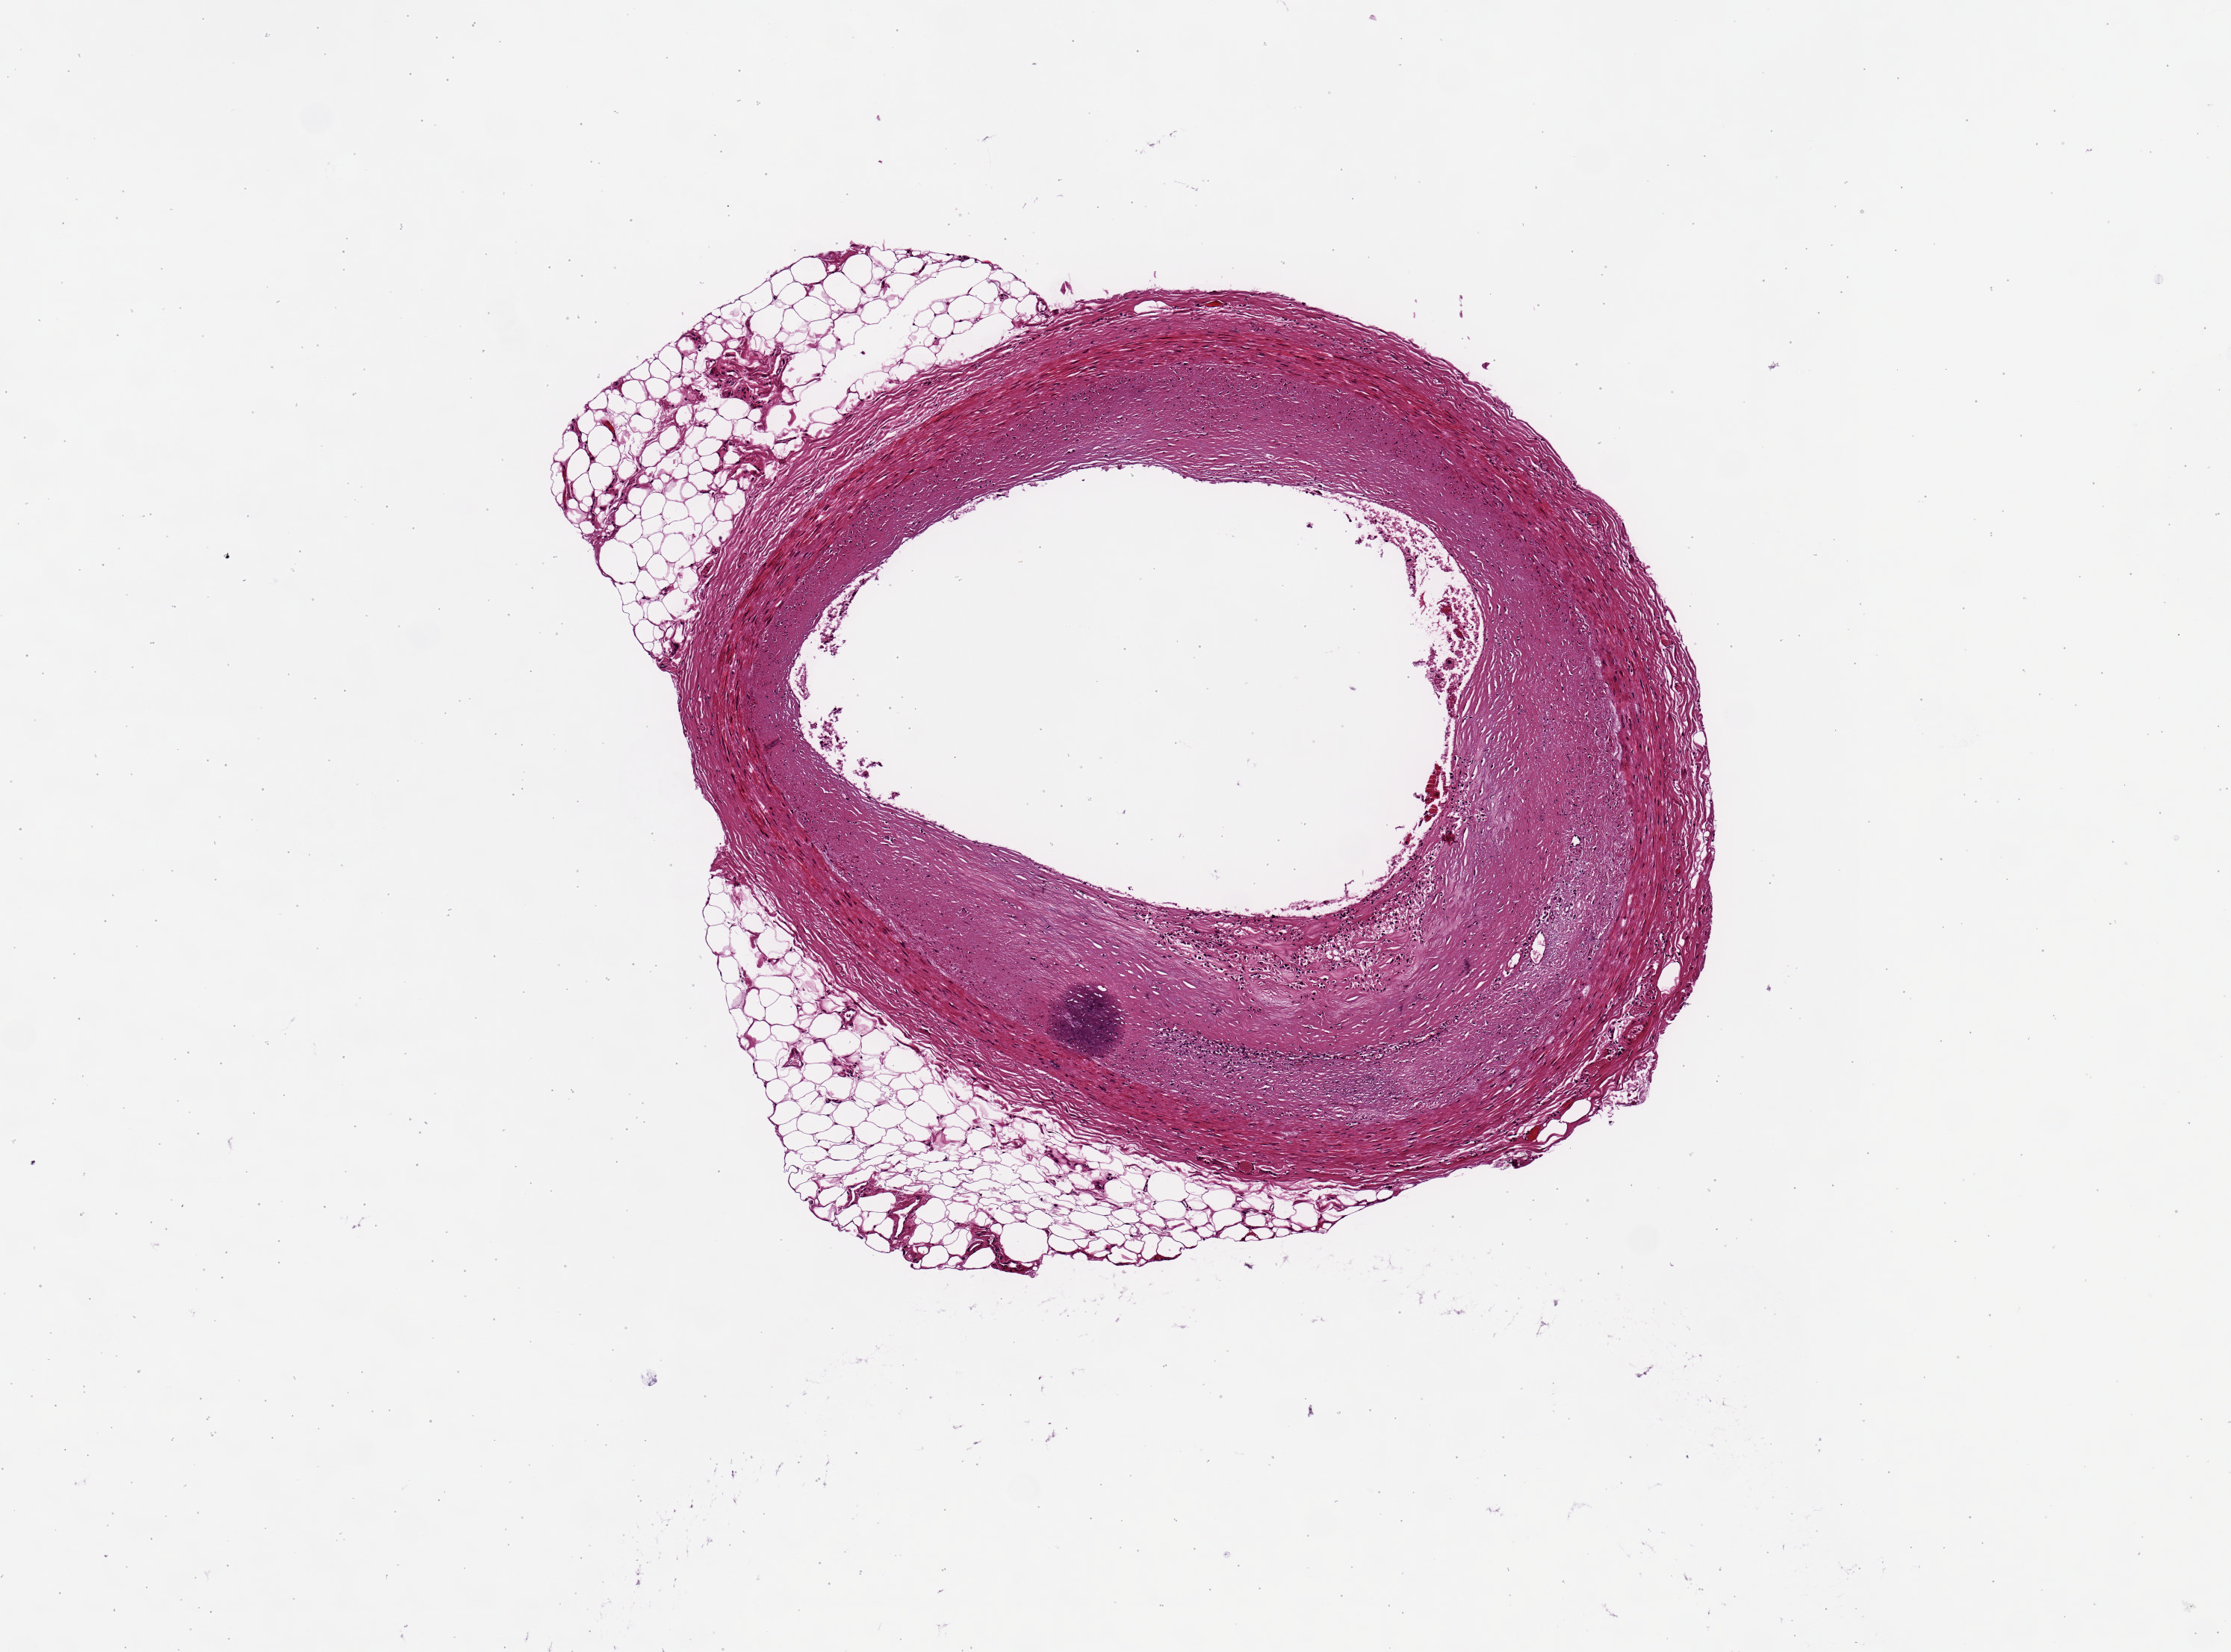
H&E whole-slide image, brightfield — low-resolution overview of the scanned area, about 5.9 x 4.4 mm (slide scanned at 20x), PAXgene-fixed paraffin-embedded (PFPE) section, target tissue: coronary artery, tissue donor sample. Donor: male.
Review note (as recorded): Eccentric atheromatous plaque, but wide lumen. Fat comprises 30% of aliquot. 2.7x2.3mm.